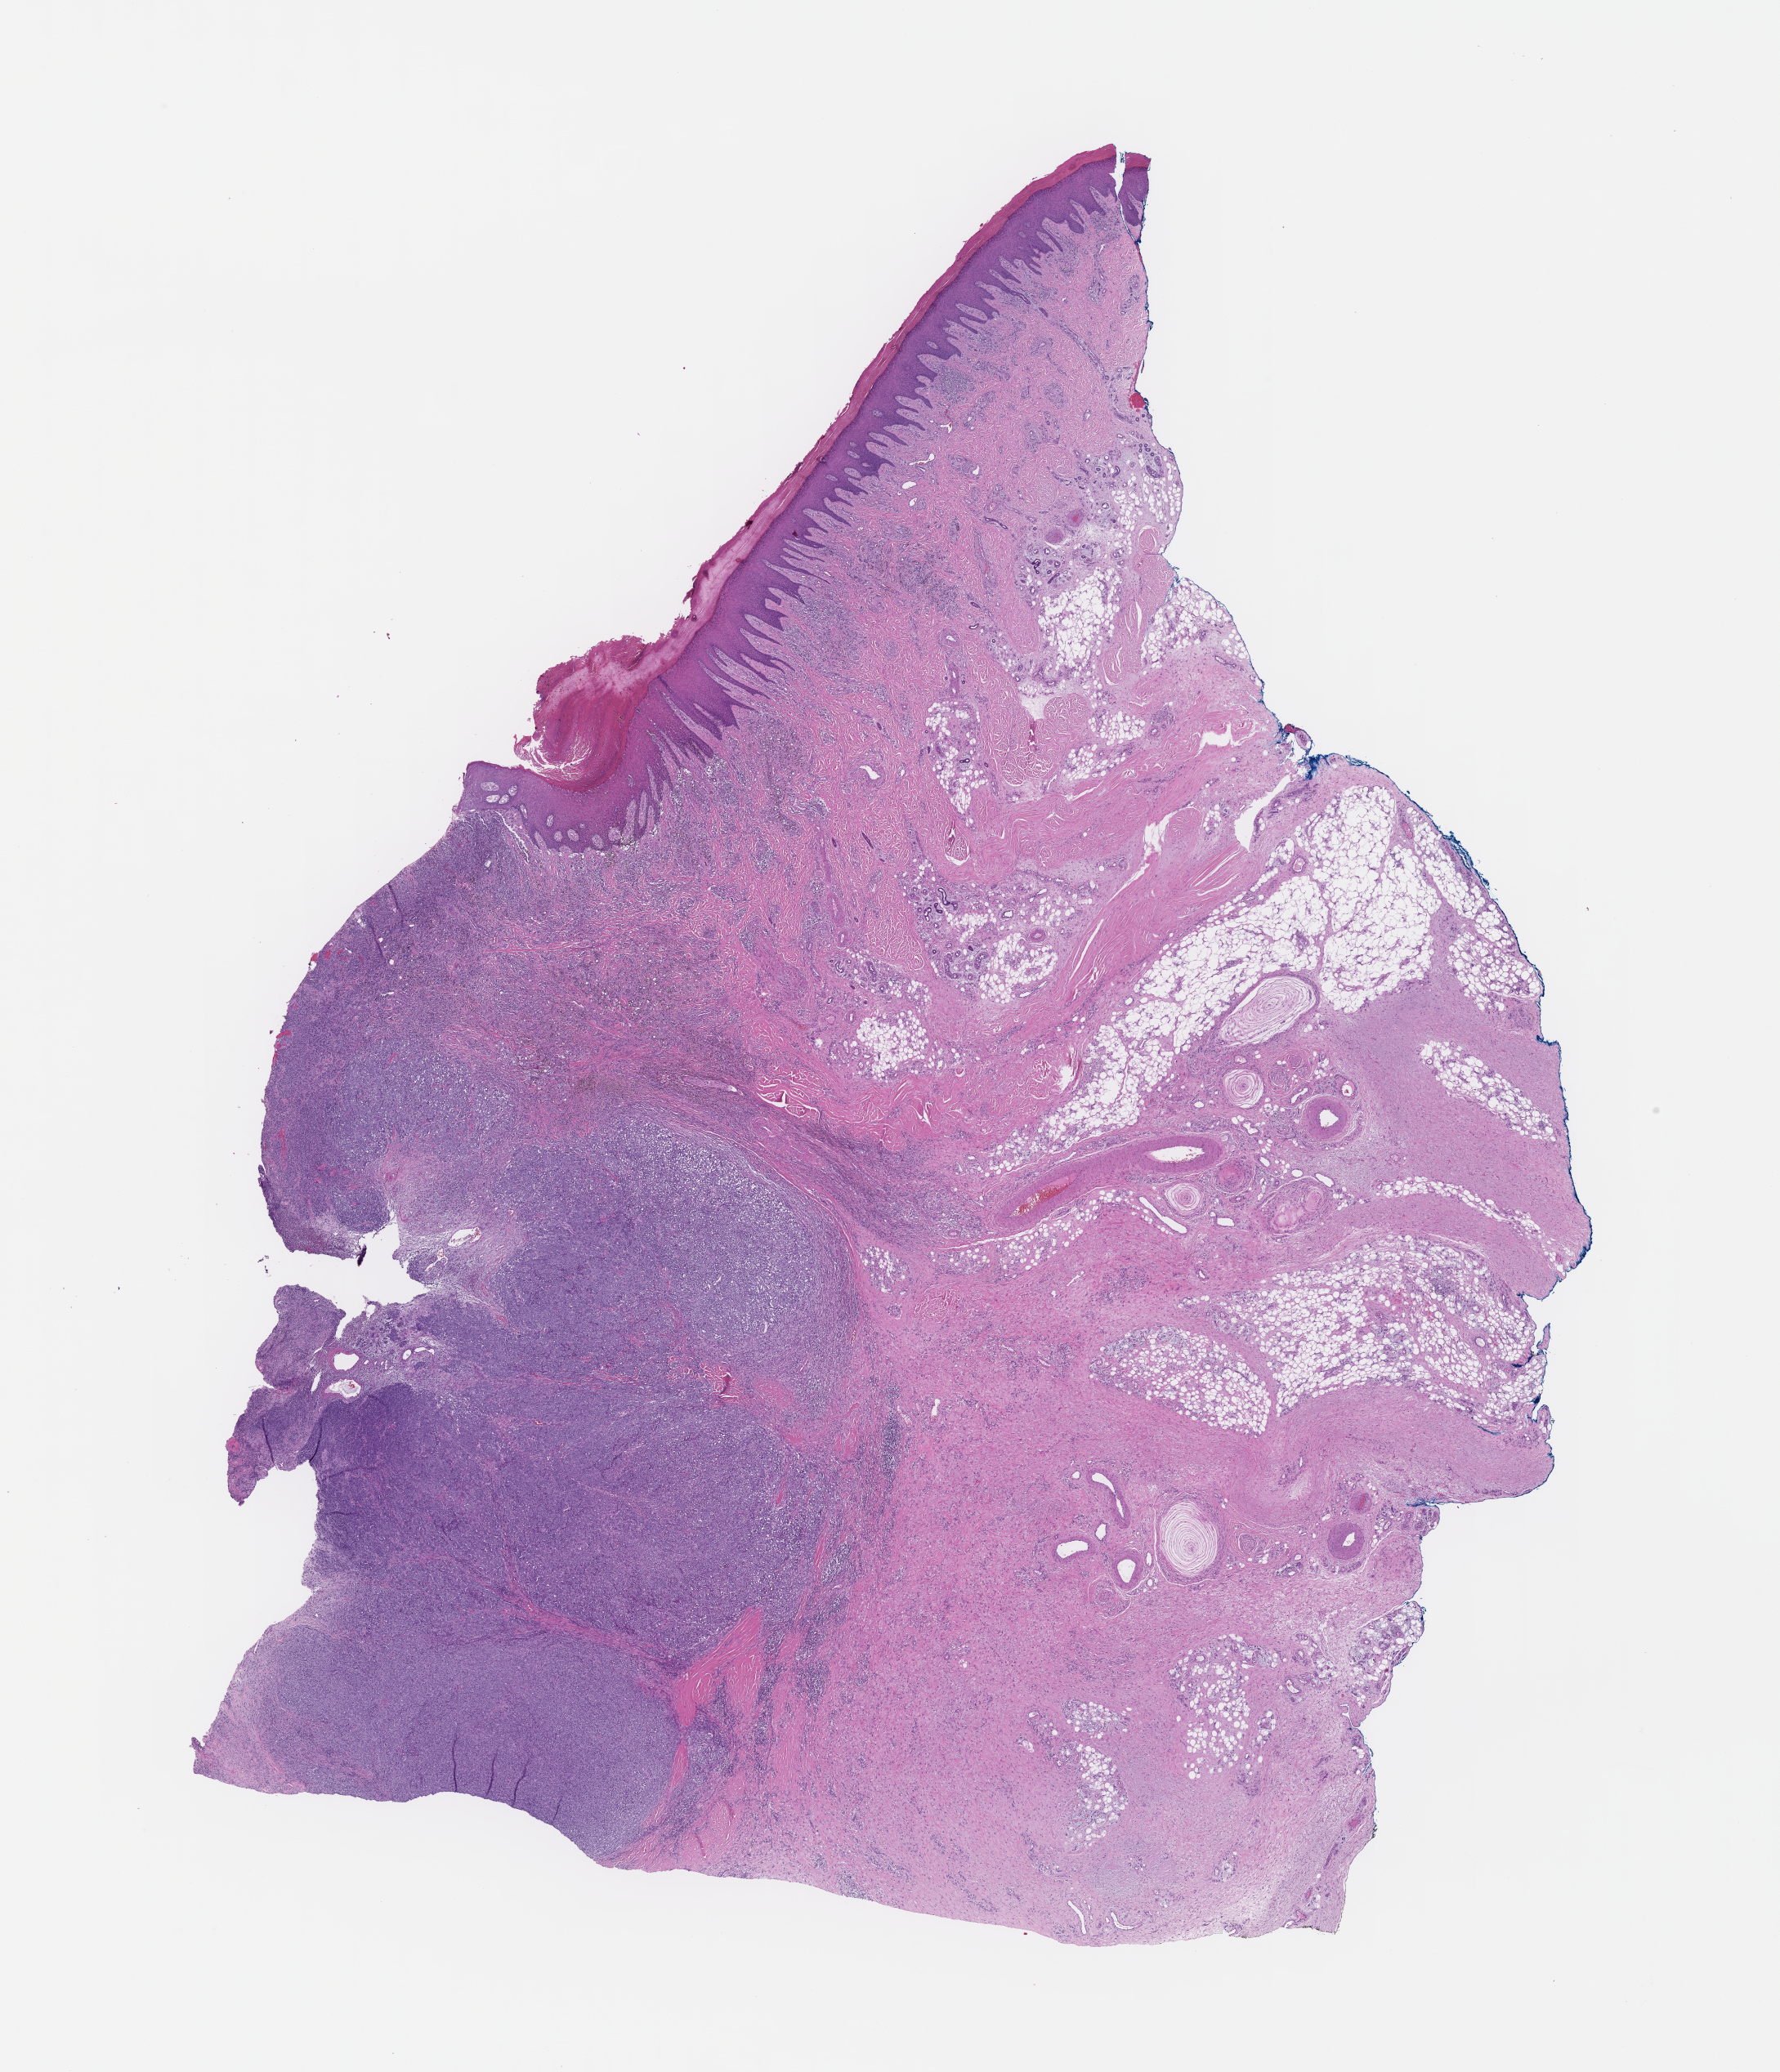
Haematoxylin and eosin whole-slide image, shown as a low-resolution overview of the whole scanned area (about 17.6 x 20.5 mm); formalin-fixed, paraffin-embedded (FFPE) tissue; tissue site: skin. Patient sex: female.
- this section: primary tumour tissue
- diagnosis: Melanoma